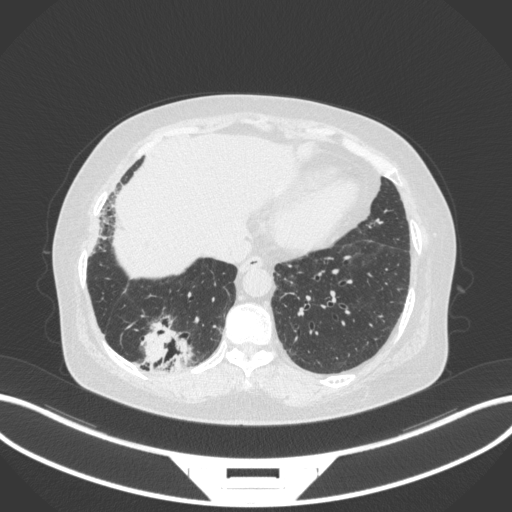
Chest CT, one axial slice; position 45 of 303 along the scan axis; reconstruction kernel B31f; 120 kVp; lung window (W 1500 / L -600 HU); 512 × 512 image matrix. Female patient, age 65 years. From the clinical record (not read from this slice): clinical TNM (as recorded): T2b N1 M0; histopathological grade: G1.
Structures marked on this image (rectangle marked by the reading radiologist):
- lung tumour (recorded histology: adenocarcinoma): bounding box [x1, y1, x2, y2] px = [138, 316, 195, 372]